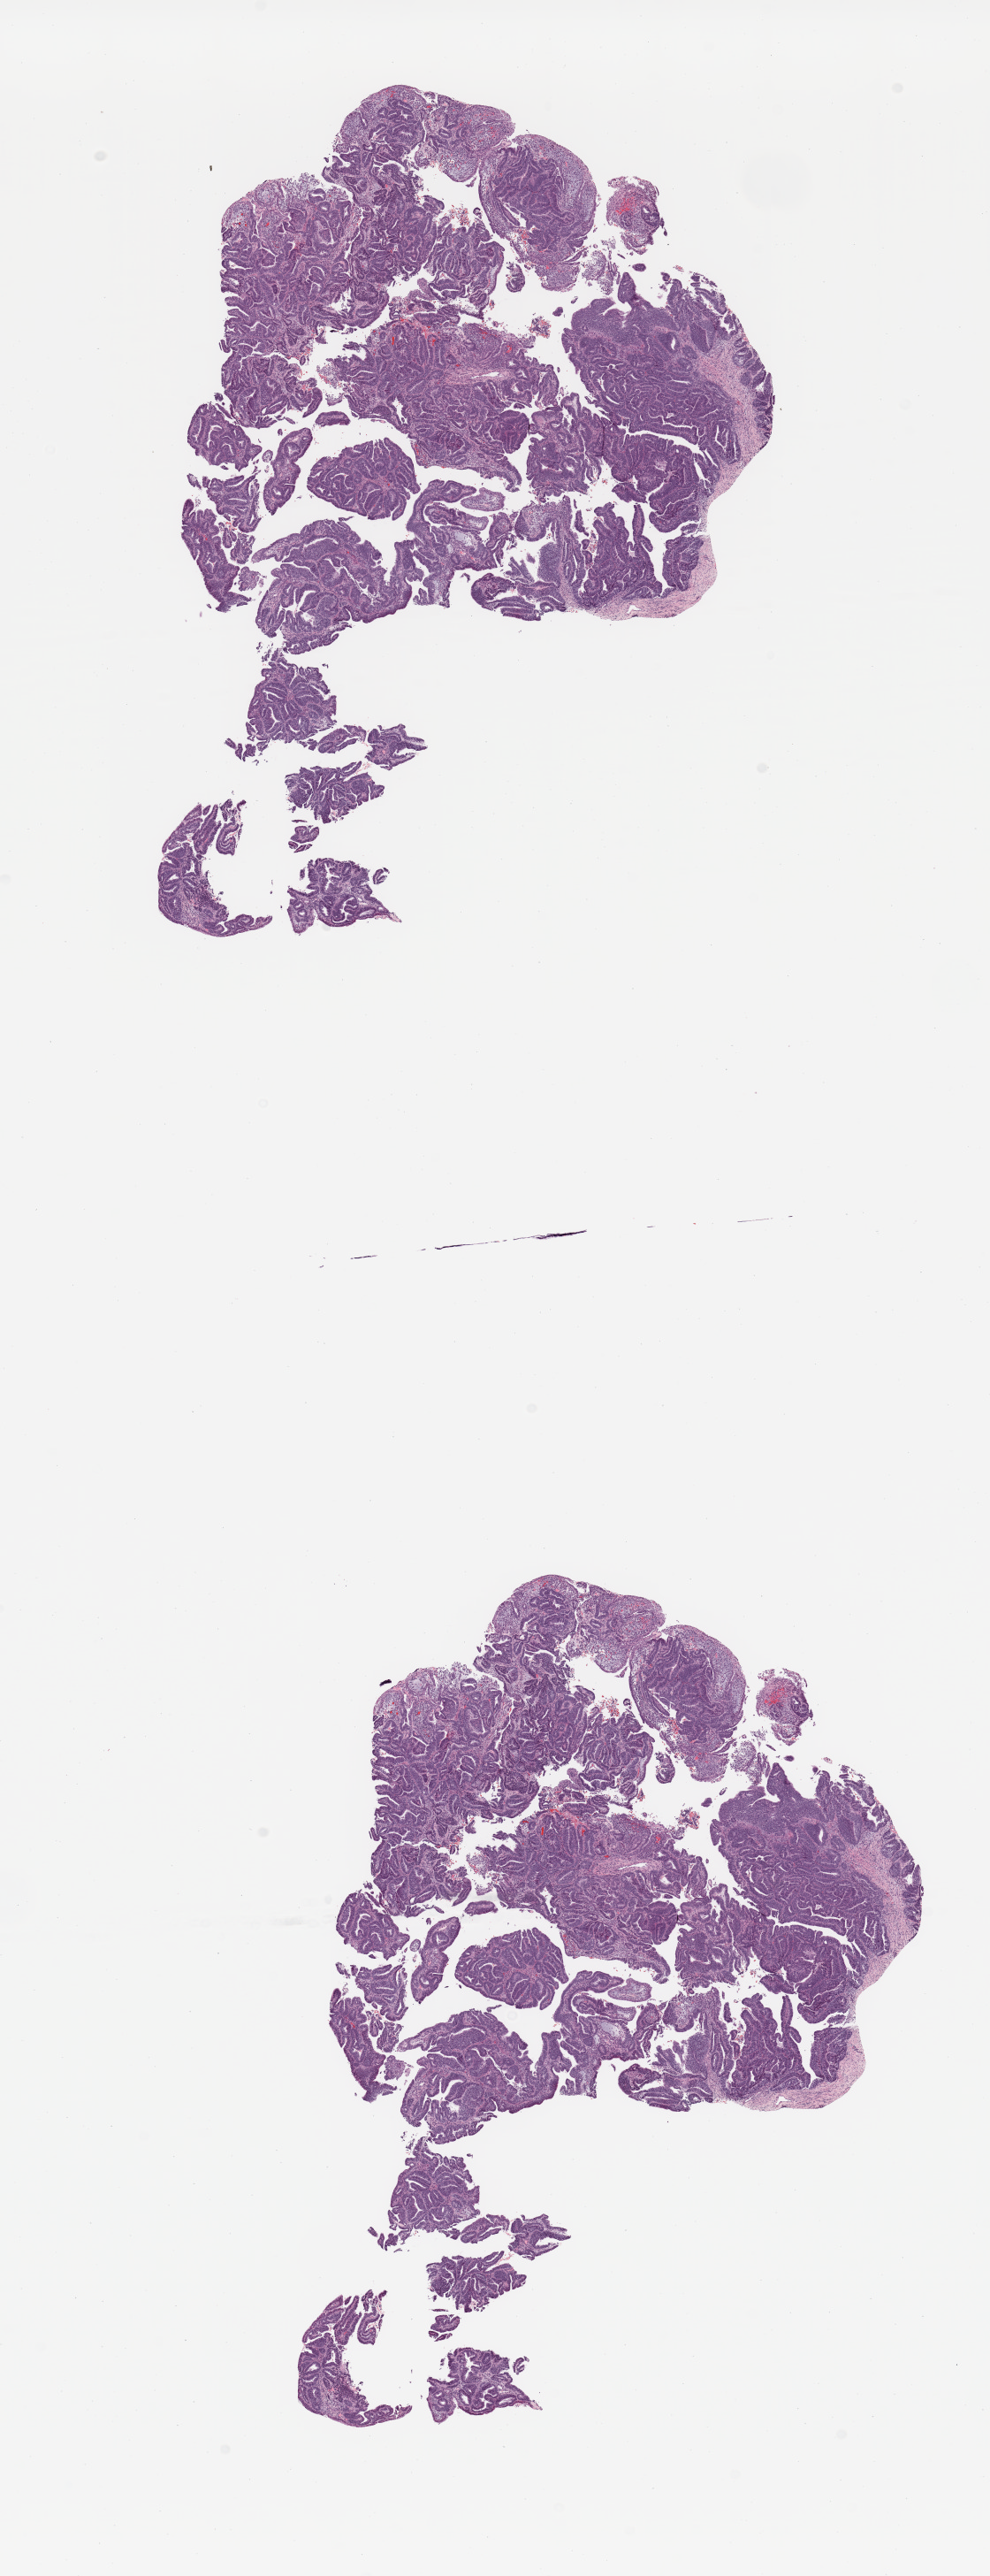
H&E-stained whole-slide image — low-resolution overview of the scanned area, about 8.9 x 23.0 mm. Tumour tissue sample, uterus. 60-year-old female patient. Histologic grade: G1 (well differentiated).
Histologic diagnosis: Endometrioid adenocarcinoma, NOS. AJCC pathologic stage: I.